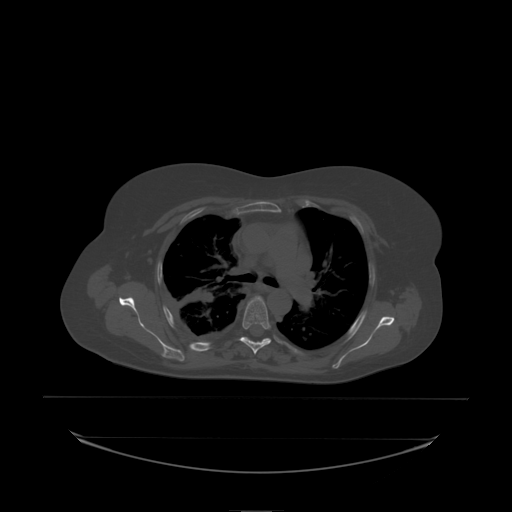
CT including the spine, one axial slice. Slice 158 of 242 in the series (ordered by position). Bone window (W 1800 / L 400 HU). 512 × 512 image matrix. Female patient, age 53 years. Case-level facts recorded for this patient, not image findings: primary cancer: lung; vertebrae with lytic lesions (as recorded): T7, L1.
Outlined on this slice (semi-automatic segmentation, software-assisted and operator-edited):
- T5 vertebra: bounding box (x1, y1, x2, y2) in pixels: (243, 297, 271, 330)